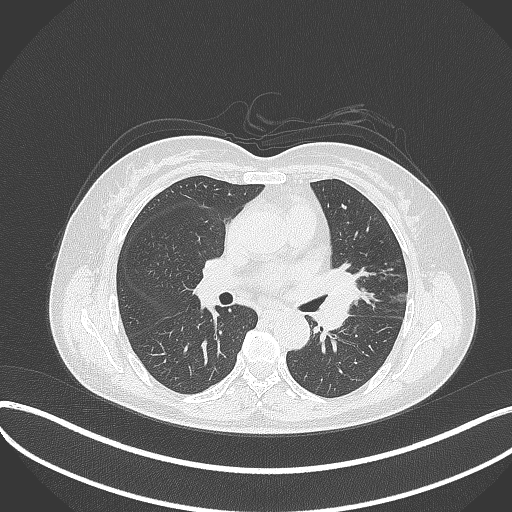
Chest CT, one axial slice; slice 193 of 373 in the series (ordered by position); reconstruction kernel B70f; 120 kVp; lung window (W 1500 / L -600 HU); 1 mm slice thickness; 512 × 512 image matrix, field of view 400 × 400 mm. Female patient, age 54 years. Case-level facts recorded for this patient, not image findings: clinical TNM (as recorded): T2a N1 M0.
Annotated regions visible in this slice (bounding box drawn by a radiologist):
- lung tumour (recorded histology: small cell carcinoma): bounding box (x1, y1, x2, y2) in pixels: (316, 267, 361, 332)